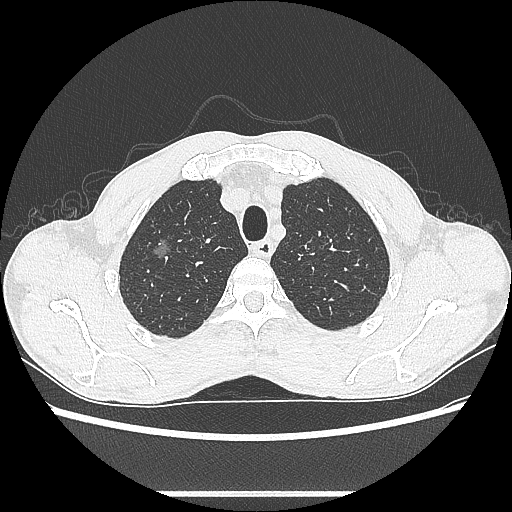
Chest CT, one axial slice; position 497 of 601 along the scan axis; lung window (W 1500 / L -600 HU); 0.62 mm slice thickness; 512 × 512 image matrix, field of view 357 × 357 mm. Male patient, age 54 years. Case-level facts recorded for this patient, not image findings: clinical TNM (as recorded): T1a N0 M0.
Outlined on this slice (rectangle marked by the reading radiologist):
- lung tumour (recorded histology: adenocarcinoma): bounding box (x1, y1, x2, y2) in pixels: (148, 233, 175, 266)